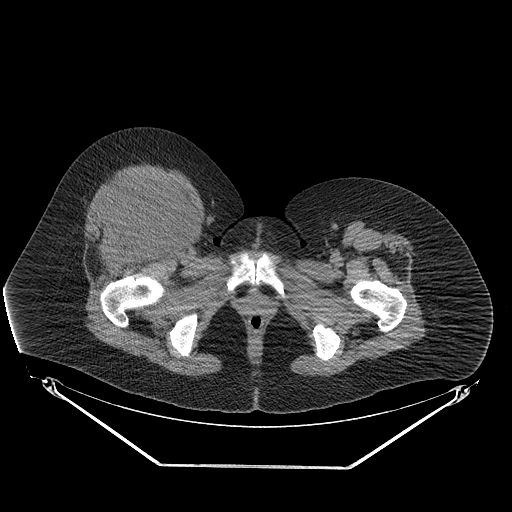
CT of an extremity soft-tissue mass (from a PET/CT study), one axial slice; slice 59 of 267 in the series (ordered by position); reconstruction kernel STANDARD; soft-tissue window (W 400 / L 40 HU); 512 × 512 image matrix. Female patient. Case-level facts recorded for this patient, not image findings: histological type: malignant solitary fibrous tumor; grade: intermediate; site of the primary tumour: right thigh.
Outlined on this slice (expert contour drawn on MRI and transferred to this co-registered scan by the dataset authors):
- gross tumour volume including surrounding oedema: bounding box (x1, y1, x2, y2) in pixels: (94, 174, 188, 243)
- gross tumour volume (mass): (96, 178, 184, 241)